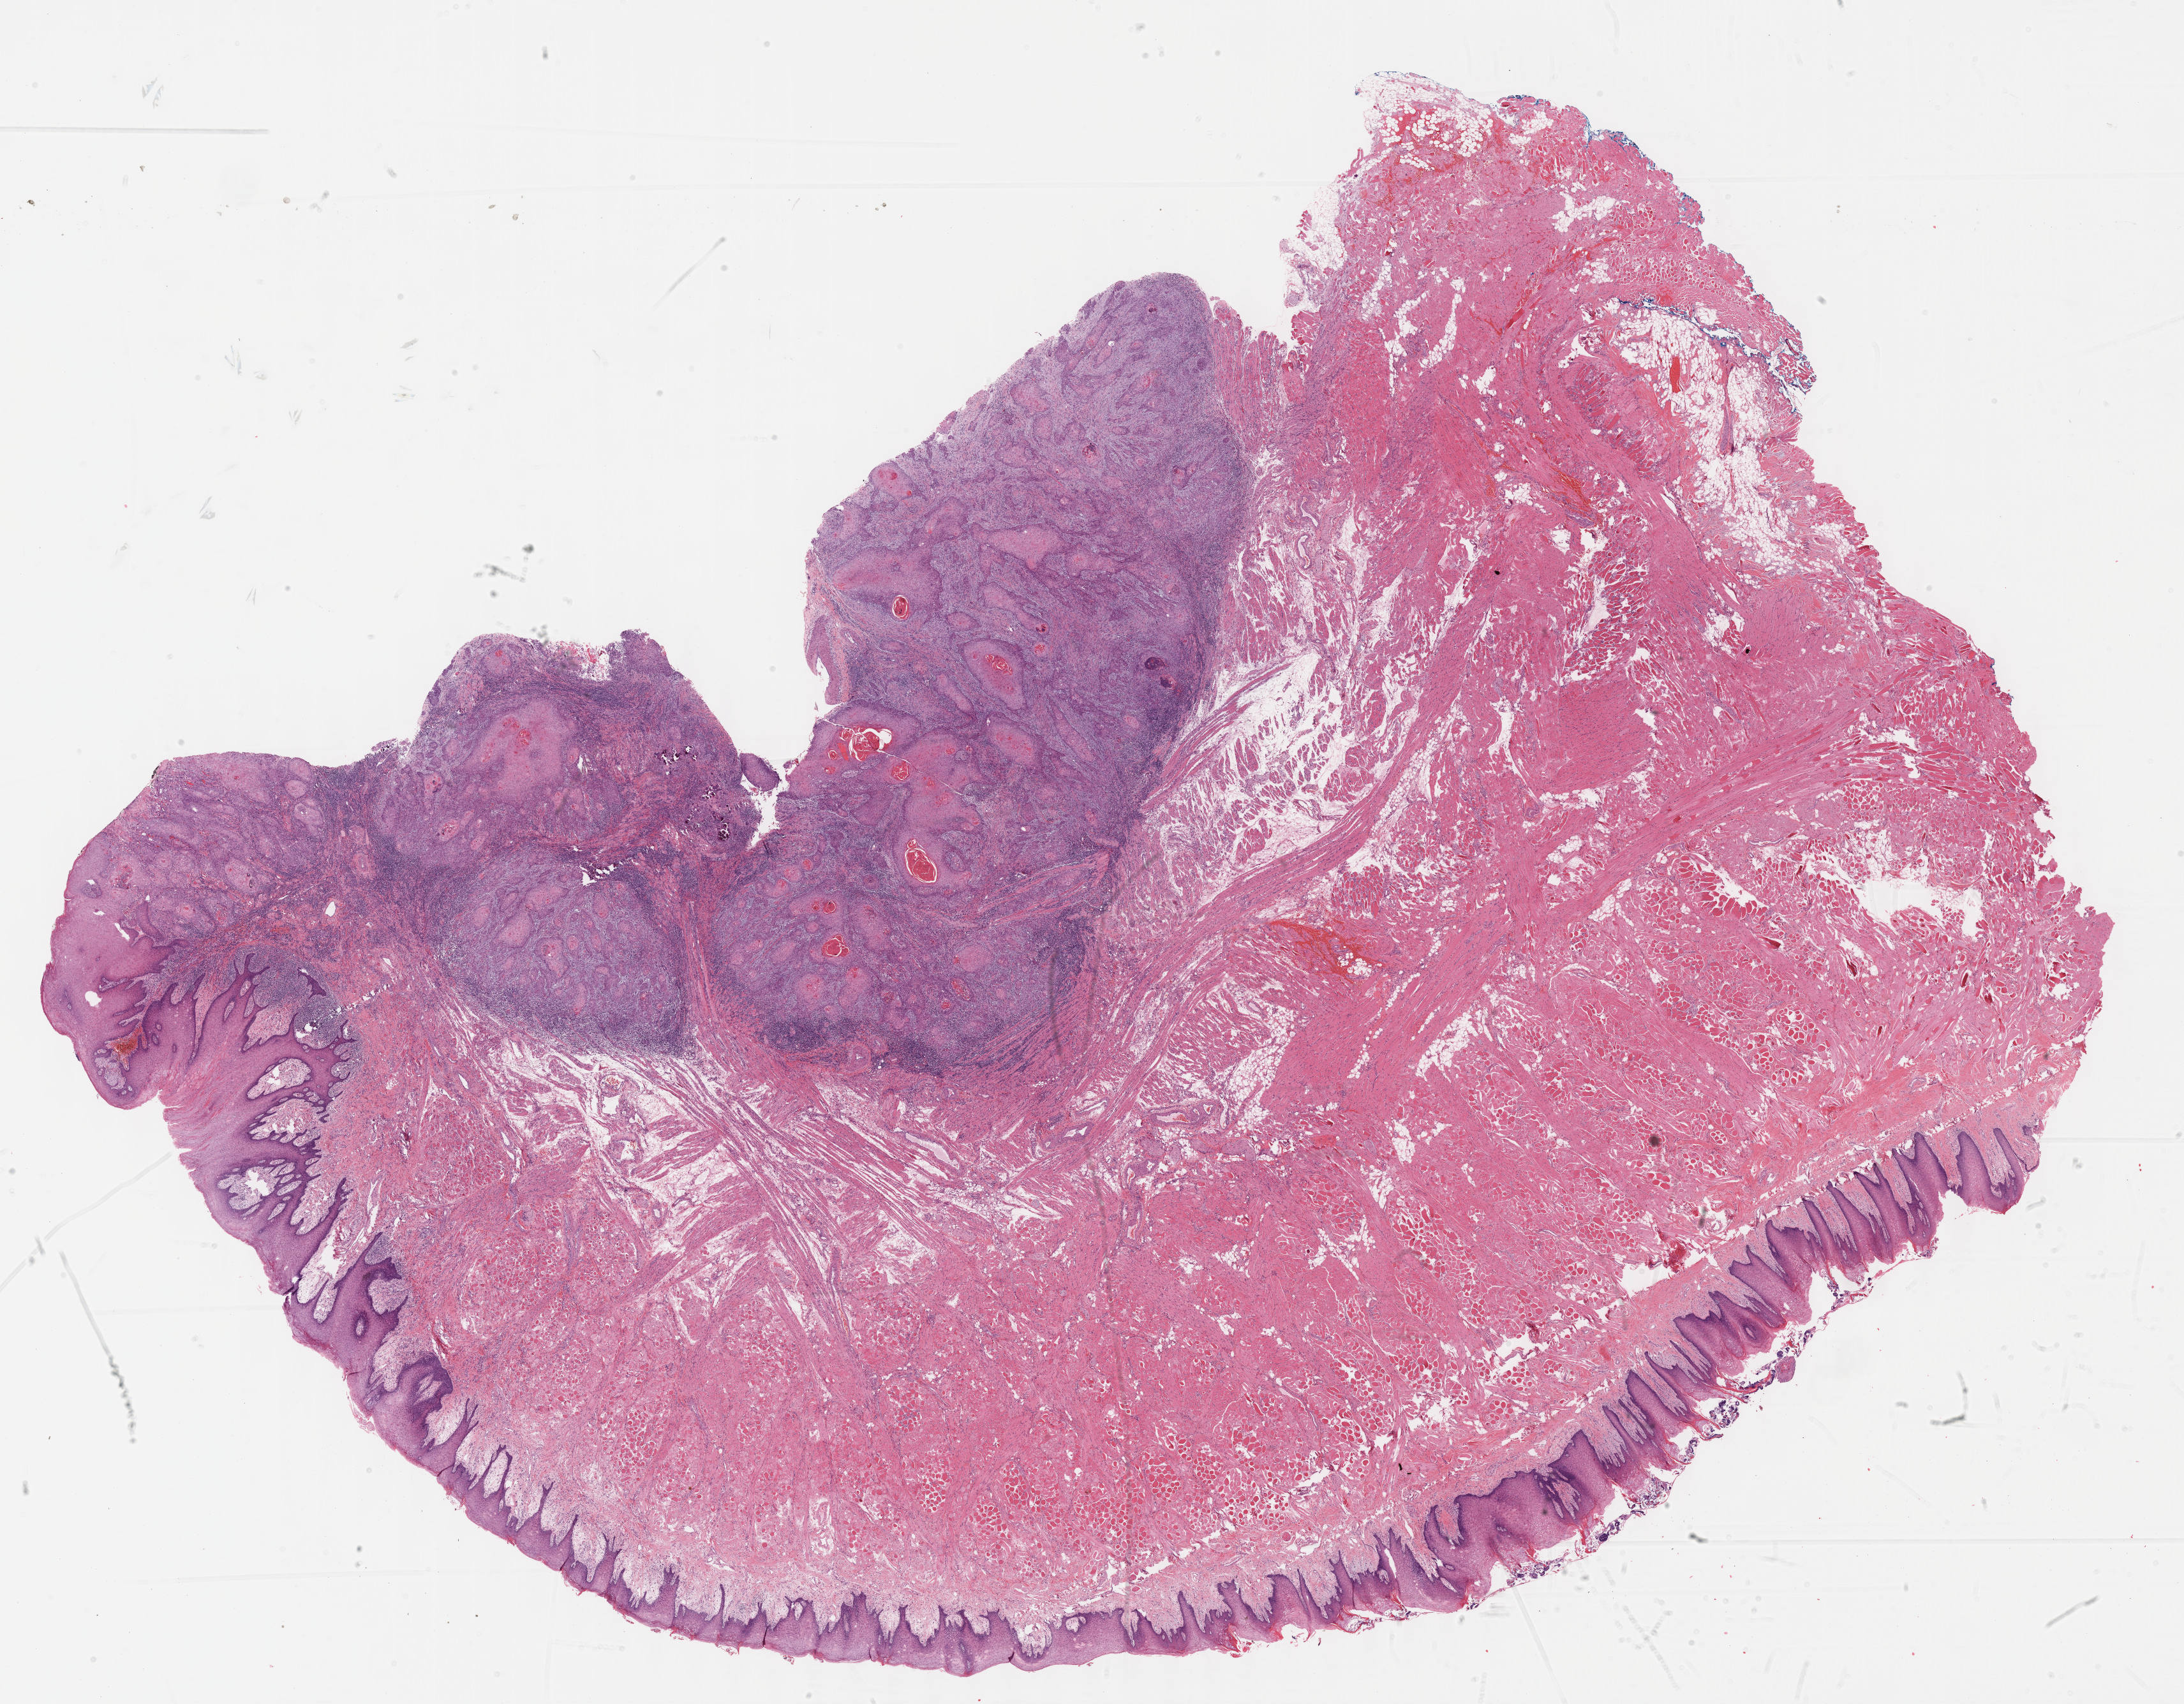
Whole-slide histology image, H&E-stained — shown as a low-resolution overview of the whole scanned area (about 27.7 x 21.6 mm); formalin-fixed paraffin-embedded (FFPE) diagnostic section; head and neck, primary tumour sample. Female patient; age at initial diagnosis 69 years. Histologic grade: G2 (moderately differentiated).
- TNM: T2 N0
- histologic diagnosis: Squamous cell carcinoma, NOS (tongue, NOS)
- AJCC pathologic stage: II (7th edition)